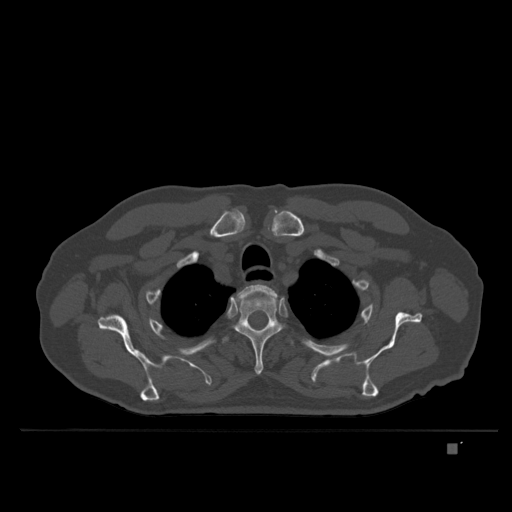
CT including the spine, one axial slice; position 301 of 435 along the scan axis; bone window (W 1800 / L 400 HU); 1.5 mm slice thickness; 512 × 512 image matrix, field of view 434 × 434 mm. Patient: male, 73 years. From the clinical record (not read from this slice): primary cancer: skin.
Annotated regions visible in this slice (semi-automatically segmented with operator editing):
- T2 vertebra: bounding box <233,283,277,309> (left, top, right, bottom; pixels)
- T3 vertebra: <235,297,282,375>
- T4 vertebra: <222,336,294,346>